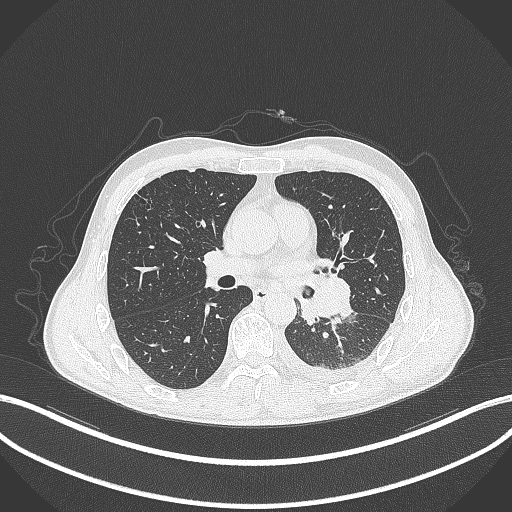
Chest CT, one axial slice; reconstruction kernel B70f; 120 kVp; lung window (W 1500 / L -600 HU); 1 mm slice thickness; 512 × 512 image matrix. Patient: male, 47 years. From the clinical record (not read from this slice): clinical TNM (as recorded): T3 N1 M1c; histopathological grade: G3.
Structures marked on this image (rectangle marked by the reading radiologist):
- lung tumour (recorded histology: small cell carcinoma): box from (x=297, y=271) to (x=359, y=328) px